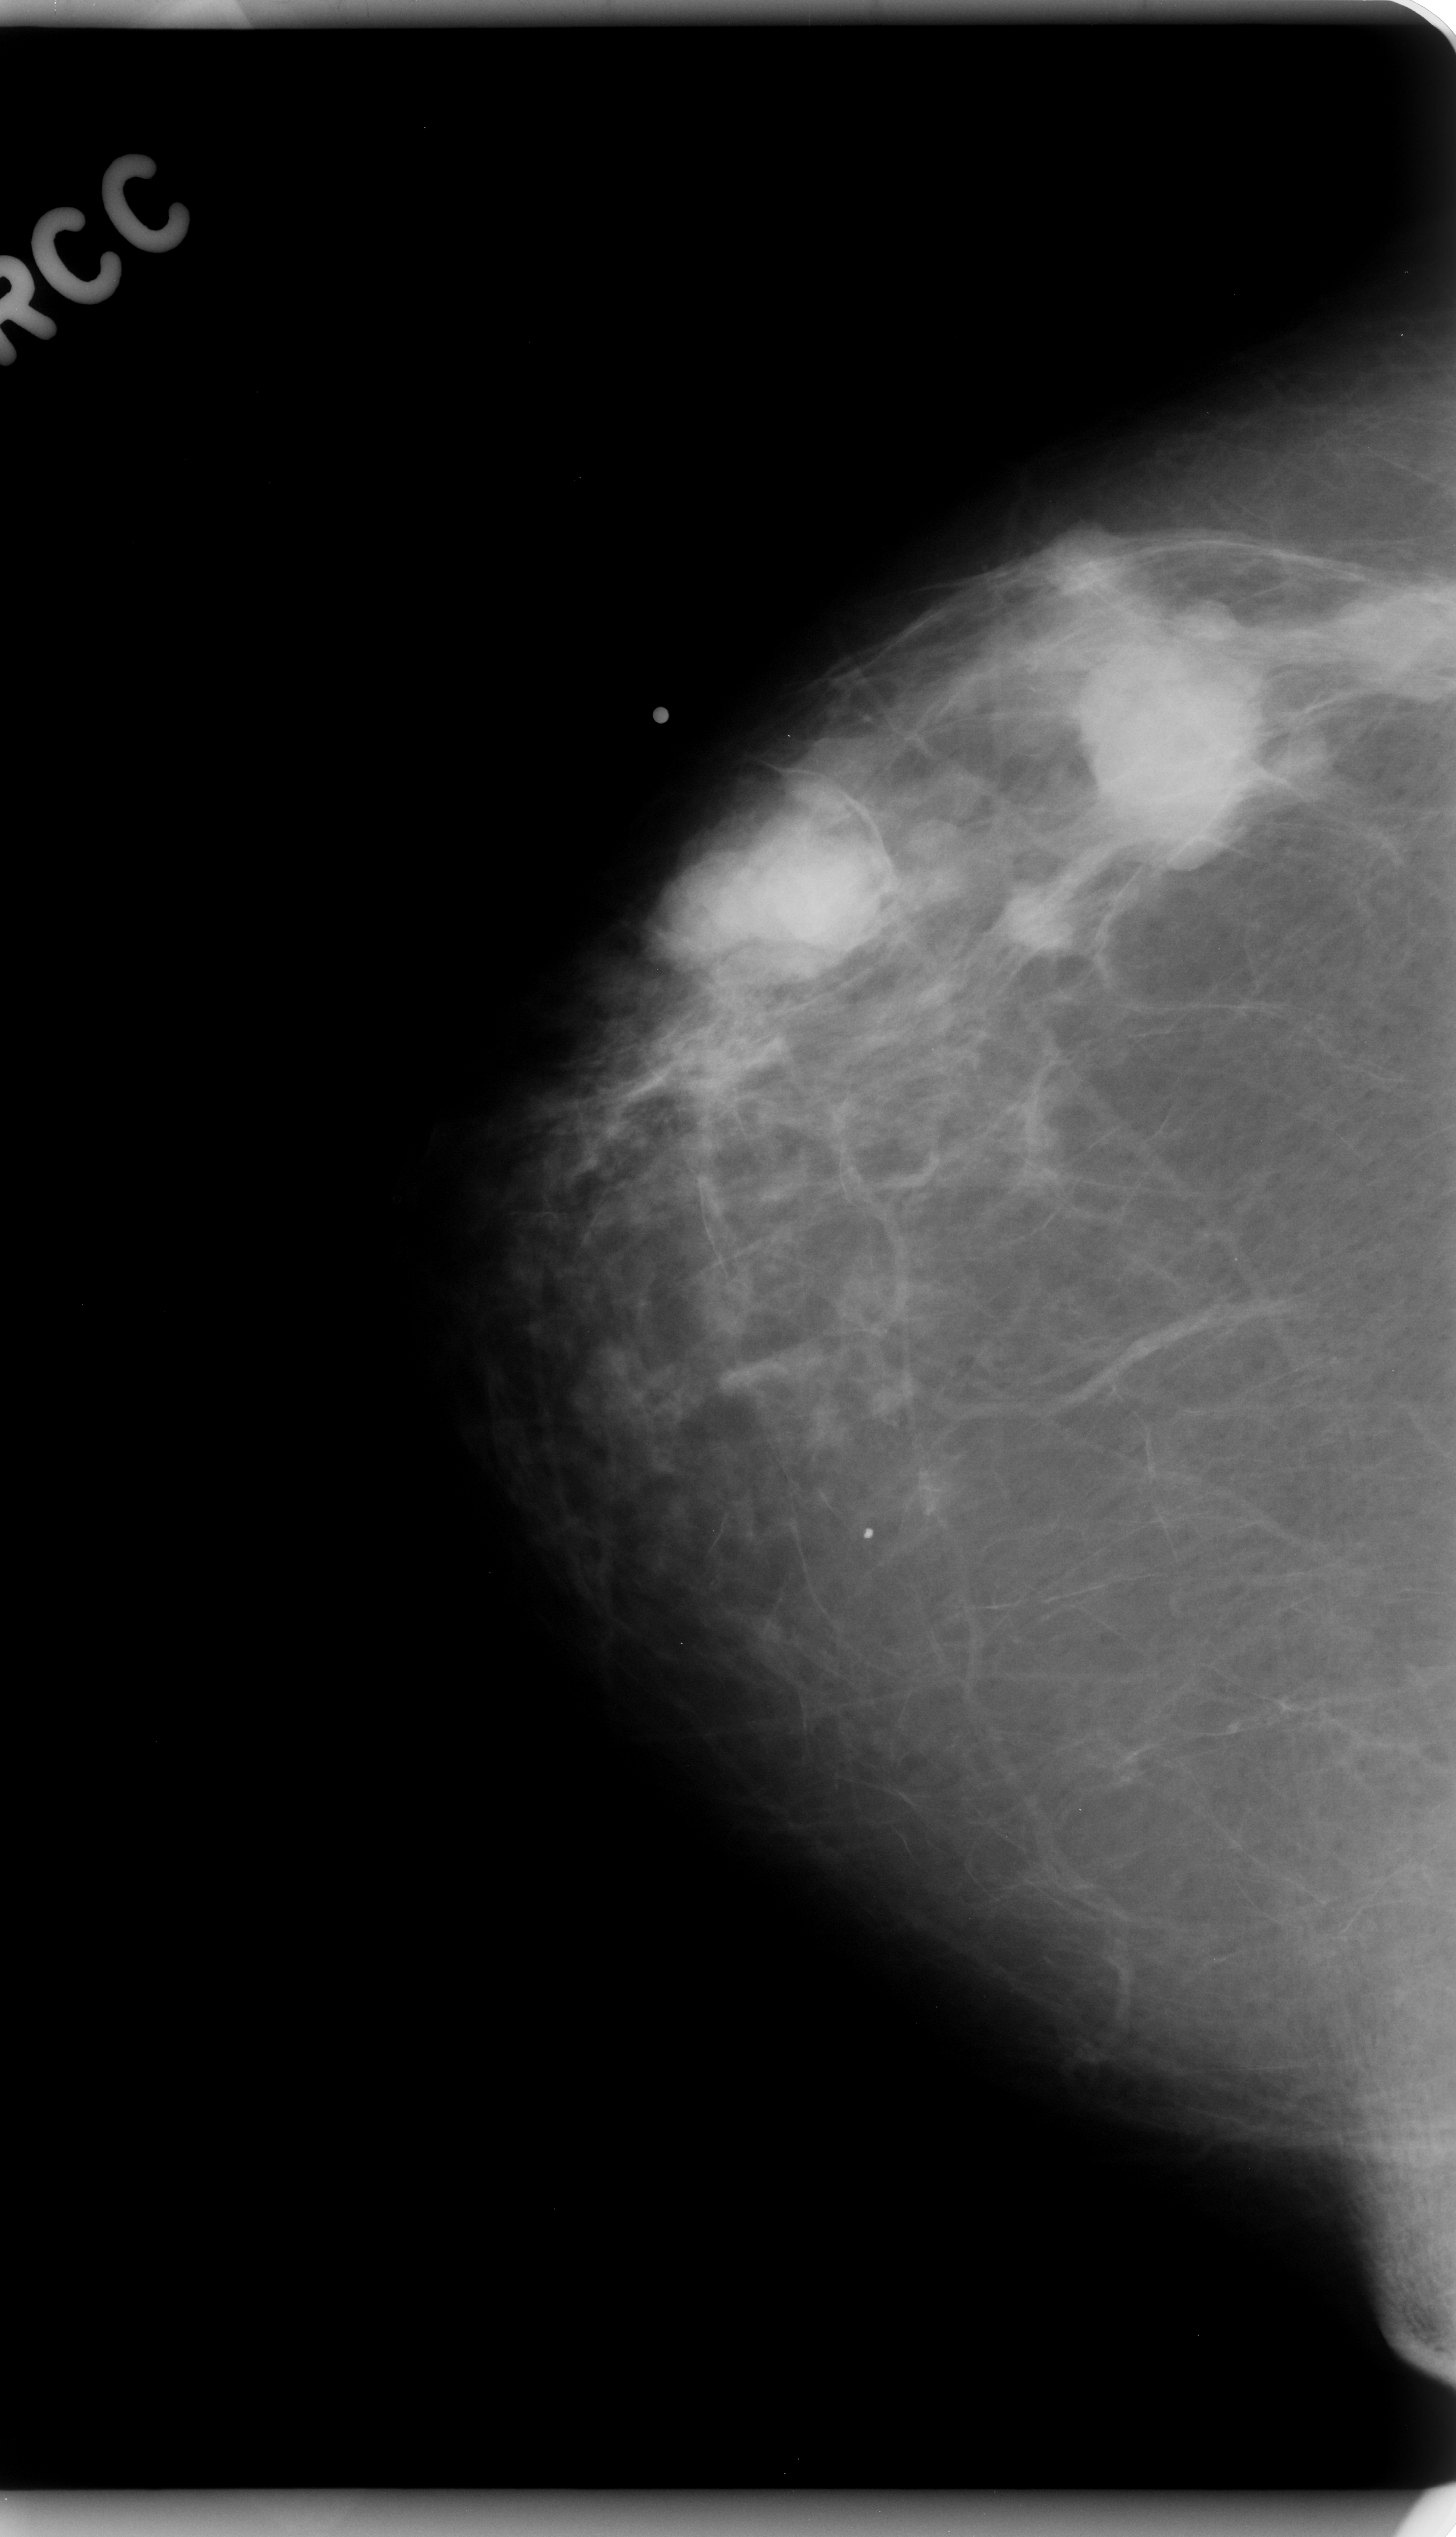
Mammogram (digitized film); right breast; craniocaudal (CC) view; BI-RADS breast density category 1 (scale 1–4).
Marked abnormality: mass, shape lobulated, margins circumscribed; BI-RADS assessment category 5; subtlety rating 5 on a 1 (subtle) to 5 (obvious) scale; pathology result (as recorded, not read from the image): malignant.